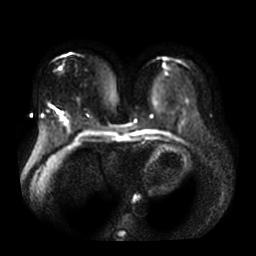
Breast MRI, one axial slice; slice 15 of 36 in the series (ordered by position); diffusion-weighted series; image 2 of 4 stored at this slice position (different b-values; order by instance number); 3 T; 5 mm slice thickness; 256 × 256 image matrix, field of view 360 × 360 mm. Female patient.
Structures marked on this image (manually delineated by an expert):
- tumour on diffusion-weighted imaging: bounding box (x1, y1, x2, y2) in pixels: (61, 117, 63, 120)